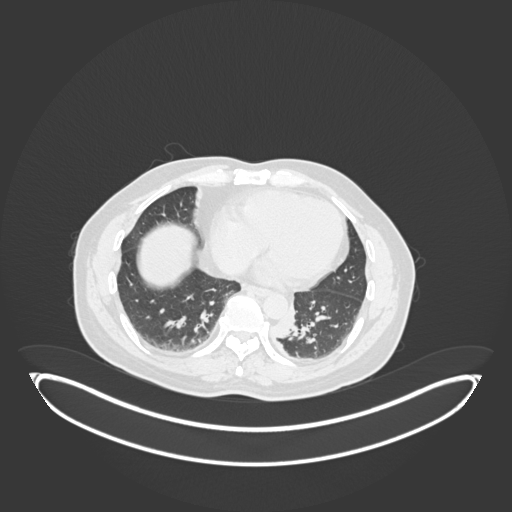
Chest CT, one axial slice. Position 54 of 258 along the scan axis. 120 kVp. Lung window (W 1500 / L -600 HU). 512 × 512 image matrix, field of view 500 × 500 mm. Patient: male, 54 years. From the clinical record (not read from this slice): clinical TNM (as recorded): T3 N0 M0.
Annotated regions visible in this slice (bounding box drawn by a radiologist):
- lung tumour (recorded histology: squamous cell carcinoma): bounding box <272,303,301,338> (left, top, right, bottom; pixels)